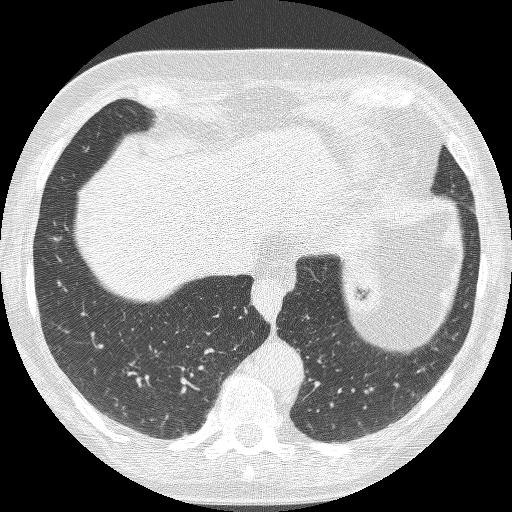
Axial slice from a low-dose chest CT screening exam, baseline screening round, lung window (W 1500 / L -600 HU), lung (sharp) reconstruction kernel (BONE), 120 kVp, slice 63 of 221 in the series, 512 × 512 image matrix. Female participant, aged 68 years at enrolment. Current smoker at enrolment.
- Expert-annotated lung lesion, bounding box <35,213,88,261> (left, top, right, bottom; pixels).
- Reader record for this screening exam (exam-level; its link to the box is not recorded): non-calcified nodule or mass ≥4 mm, right lower lobe, 16 × 12 mm, poorly defined margins, ground glass attenuation.
- Participant outcome: lung cancer diagnosed 406 days after this screen (after the second annual screen) — bronchiolo-alveolar adenocarcinoma, NOS, right lower lobe, well differentiated (G1), stage IA (AJCC 6th edition), 13 mm at pathology.